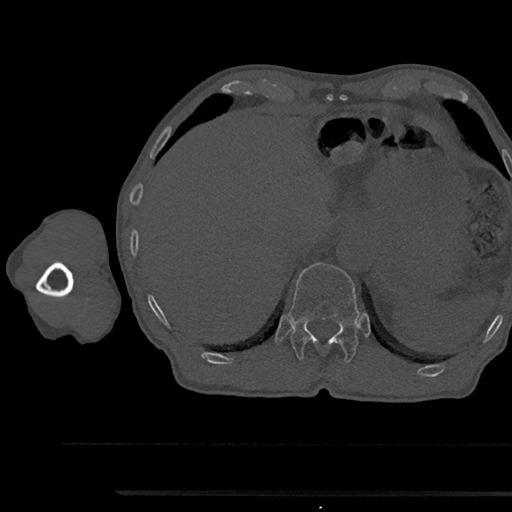
CT including the spine, one axial slice. Slice 730 of 797 in the series (ordered by position). Reconstruction kernel Br40s/3. 120 kVp. Bone window (W 1800 / L 400 HU). 512 × 512 image matrix, field of view 367 × 367 mm. Patient: male, 79 years. Case-level facts recorded for this patient, not image findings: primary cancer: prostate.
Annotated regions visible in this slice (semi-automatically segmented with operator editing):
- T12 vertebra: bounding box [x1, y1, x2, y2] px = [288, 262, 359, 362]